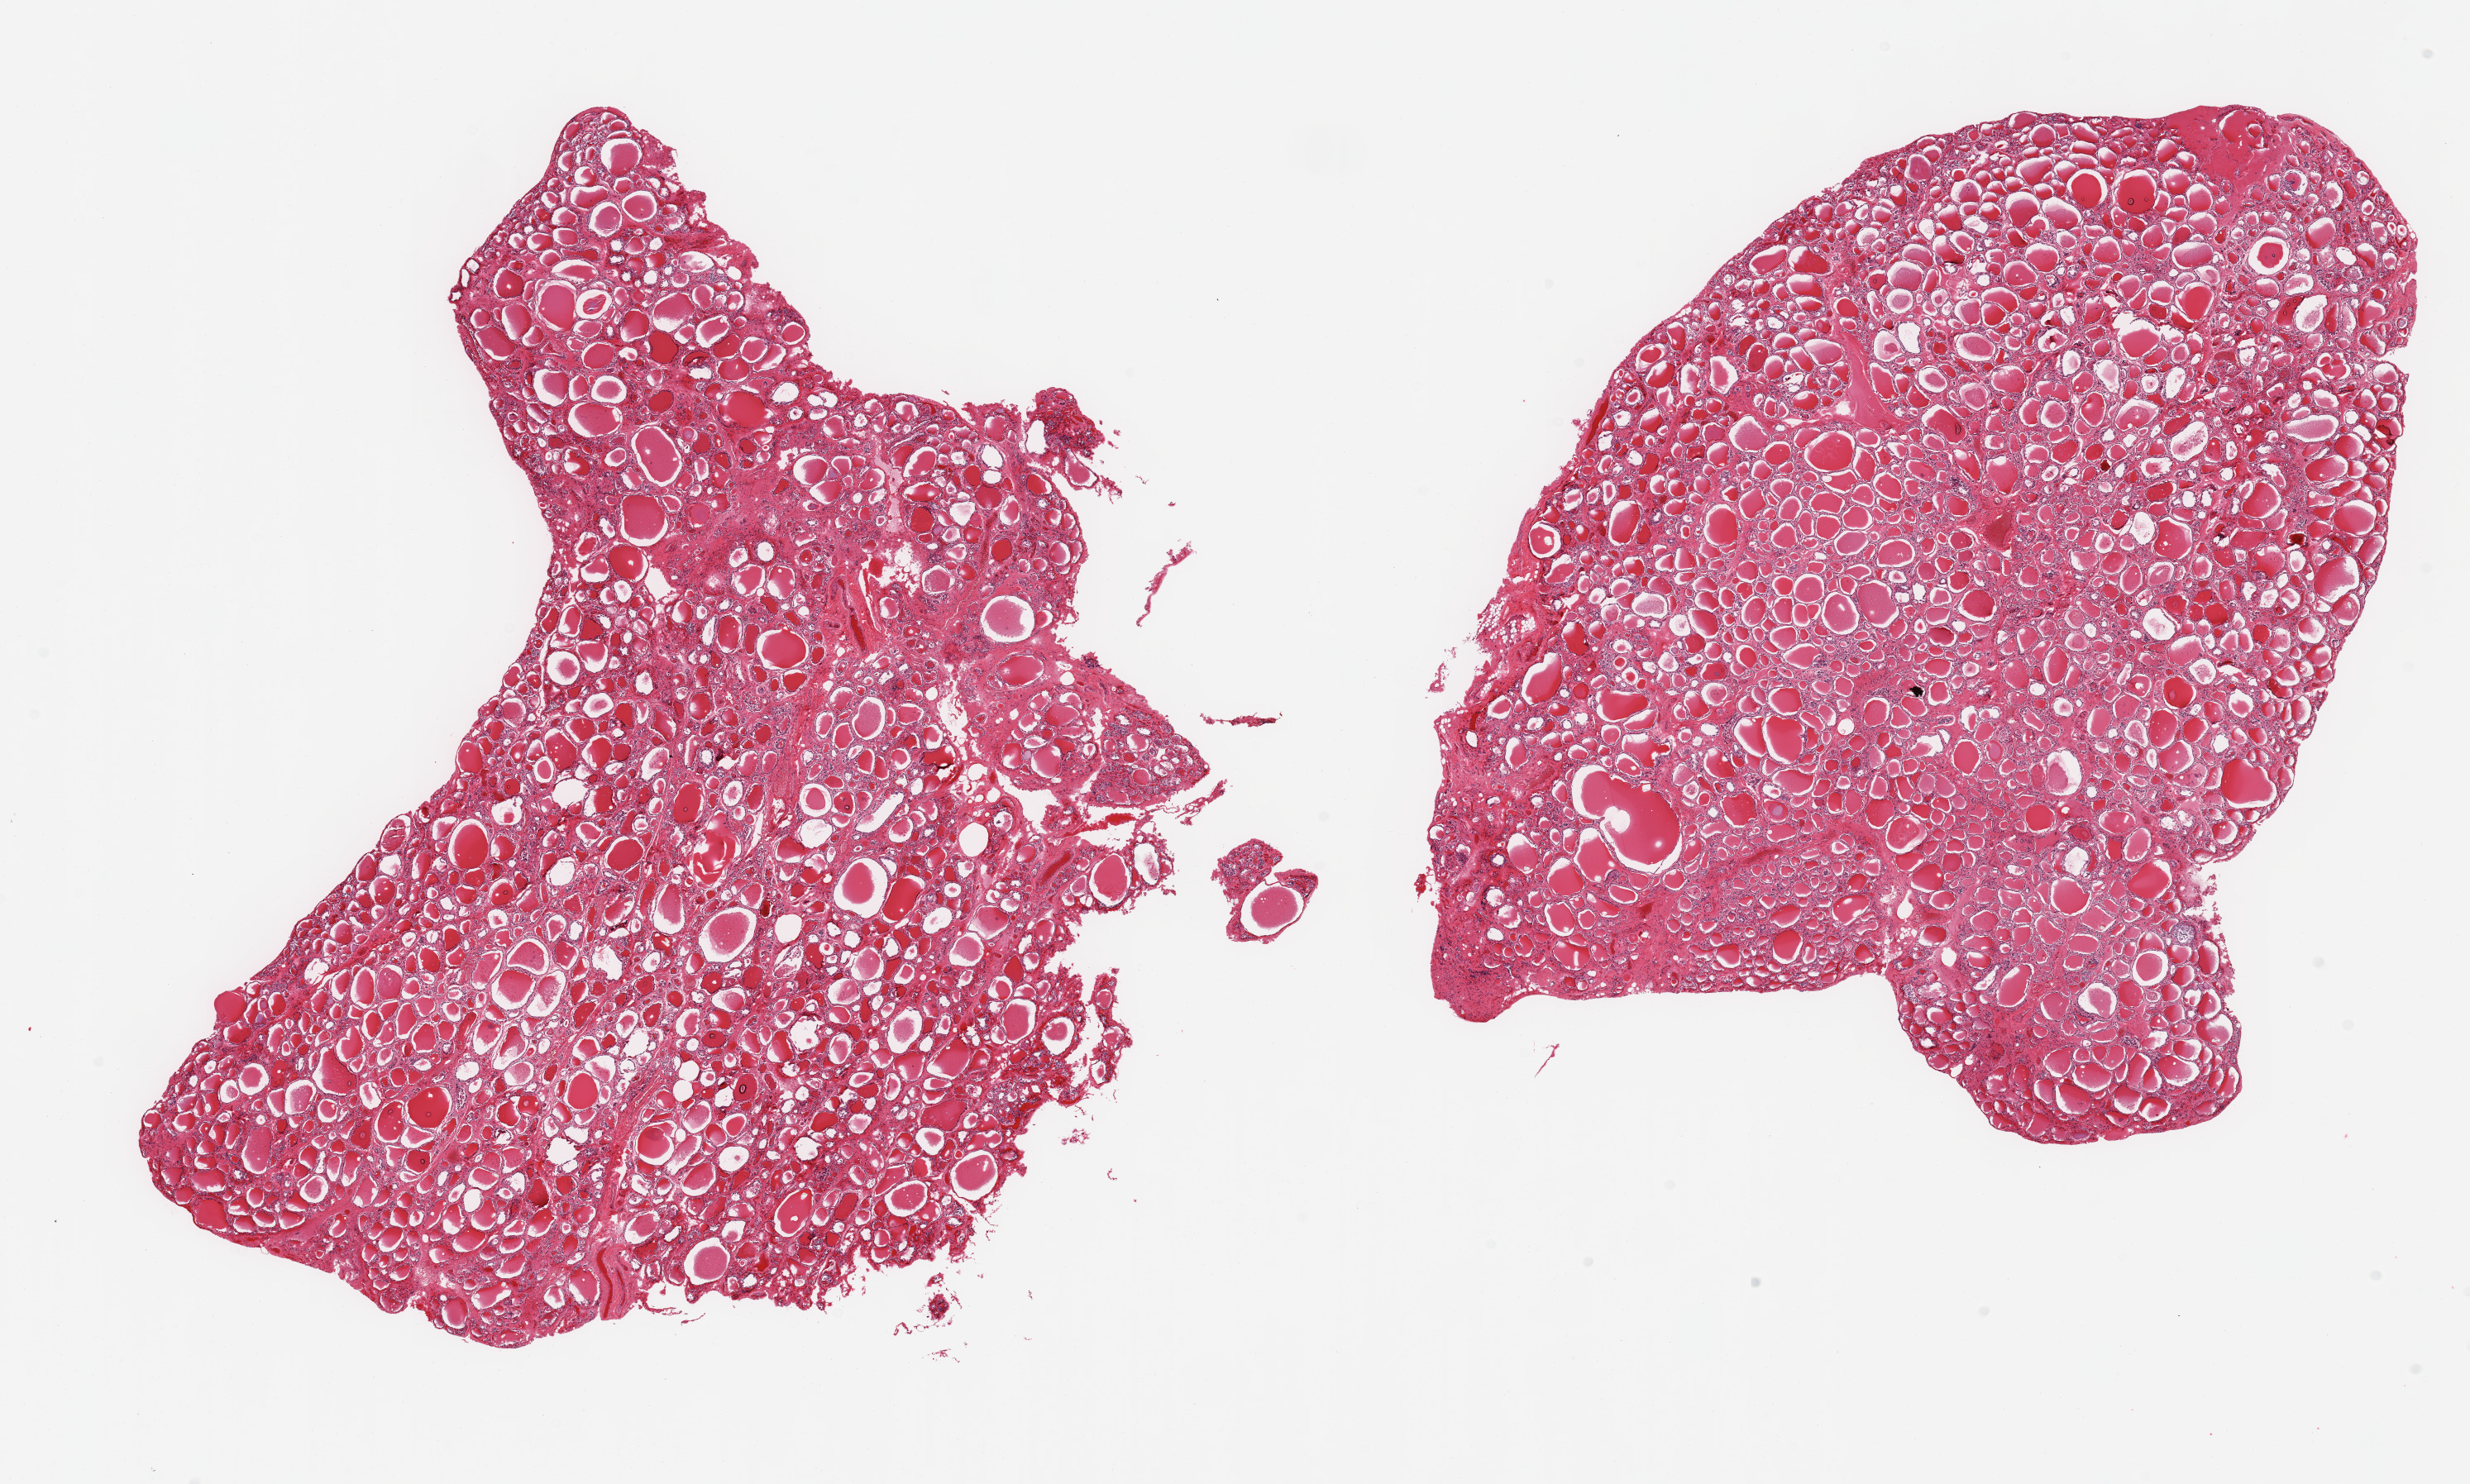
H&E whole-slide image, brightfield, low-resolution overview of the scanned area, about 23.6 x 14.2 mm (slide scanned at 20x). PAXgene-fixed, paraffin-embedded tissue. Section of thyroid (target tissue). Tissue donor sample. Donor: male.
Review note (as recorded): 2 pieces, no abnomormalities.